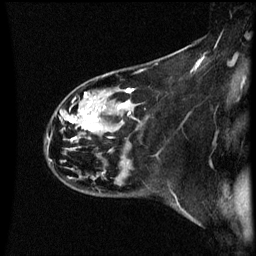
Breast MRI (dynamic contrast-enhanced), one sagittal slice; position 42 of 60 along the scan axis; dynamic contrast-enhanced series, image 2 of 3 at this slice position (ordered by acquisition); 1.5 T; TE 4.2 ms, TR 8.9 ms; 2 mm slice thickness; 256 × 256 image matrix, field of view 200 × 200 mm. Patient: female, 44 years. From the clinical record (not read from this slice): setting: breast cancer imaged before/during neoadjuvant chemotherapy; receptor status: HR-positive, HER2-negative.
Outlined on this slice (semi-automatically segmented with operator editing):
- analysis volume of interest (the breast-tissue region the enhancement analysis was run in; not a lesion): bounding box <45,78,148,189> (left, top, right, bottom; pixels)
- tumour enhancement mask (voxels above the 70 % enhancement threshold inside the analysis volume of interest): <70,90,132,141>